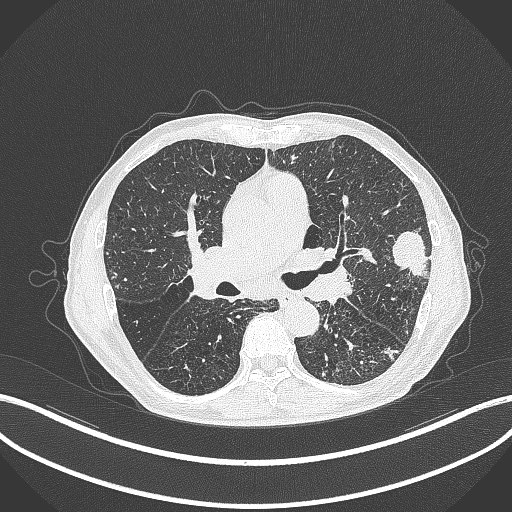
Chest CT, one axial slice. Position 237 of 463 along the scan axis. Reconstruction kernel B70f. Lung window (W 1500 / L -600 HU). 1 mm slice thickness. 512 × 512 image matrix. Male patient, age 74 years. From the clinical record (not read from this slice): clinical TNM (as recorded): T2a N1 M0.
Structures marked on this image (rectangle marked by the reading radiologist):
- lung tumour (recorded histology: adenocarcinoma): bounding box [x1, y1, x2, y2] px = [387, 229, 431, 282]